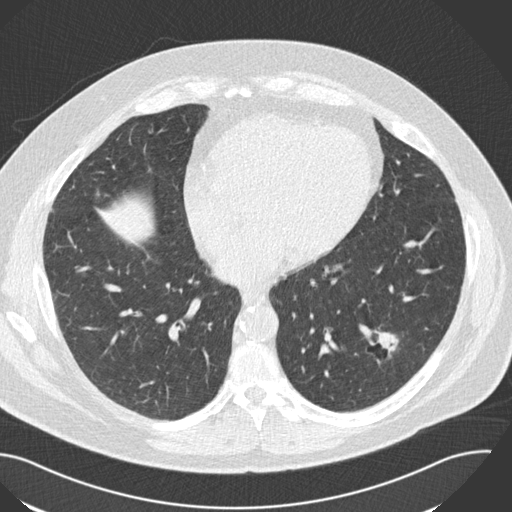
Low-dose screening chest CT, axial slice. Third screening round (two years after baseline). Lung window (W 1500 / L -600 HU). Standard (soft-tissue) reconstruction kernel (B30f). 120 kVp. Slice 82 of 153 in the series. Male, age 57 years at enrolment. Current smoker at enrolment.
Expert reader's lesion annotation, bounding box <349,316,417,372> (left, top, right, bottom; pixels). The exam's reader record, not a measurement of the box and not confirmed to be the same lesion: non-calcified nodule or mass ≥4 mm, left lower lobe, 22 × 18 mm, poorly defined margins, soft tissue attenuation, pre-existing on the prior screen: yes; interval growth: yes. Official screen result: positive, other. Participant outcome: lung cancer diagnosed 124 days after this screen — squamous cell carcinoma, NOS, left lower lobe, moderately differentiated (G2), stage IA (AJCC 6th edition), 22 mm at pathology.